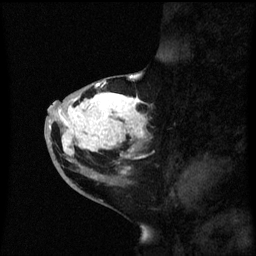
Breast MRI (dynamic contrast-enhanced), one sagittal slice; slice 26 of 60 in the series (ordered by position); dynamic contrast-enhanced series, image 2 of 3 at this slice position (ordered by acquisition); 1.5 T; TE 4.2 ms, TR 8.4 ms; 2.3 mm slice thickness; 256 × 256 image matrix, field of view 200 × 200 mm. Female patient, age 46 years. Case-level facts recorded for this patient, not image findings: setting: breast cancer imaged before/during neoadjuvant chemotherapy; receptor status: HER2-positive.
Outlined on this slice (semi-automatically segmented with operator editing):
- analysis volume of interest (the breast-tissue region the enhancement analysis was run in; not a lesion): bounding box [x1, y1, x2, y2] px = [44, 86, 153, 171]
- tumour enhancement mask (voxels above the 70 % enhancement threshold inside the analysis volume of interest): [54, 86, 145, 171]